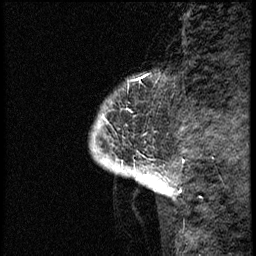
Breast MRI (dynamic contrast-enhanced), one sagittal slice. Position 3 of 68 along the scan axis. Dynamic contrast-enhanced study with each time point stored as its own series, time point 2 of 3 at this slice position (early post-contrast, ordered by acquisition time). 1.5 T. TE 4.2 ms, TR 17.6 ms. 2 mm slice thickness. 256 × 256 image matrix. Female patient, age 52 years. Case-level facts recorded for this patient, not image findings: setting: breast cancer imaged before/during neoadjuvant chemotherapy; receptor status: HER2-positive.
Outlined on this slice (semi-automatic segmentation, software-assisted and operator-edited):
- analysis volume of interest (the breast-tissue region the enhancement analysis was run in; not a lesion): bounding box <90,72,176,184> (left, top, right, bottom; pixels)
- tumour enhancement mask (voxels above the 100 % enhancement threshold inside the analysis volume of interest): <104,74,160,182>